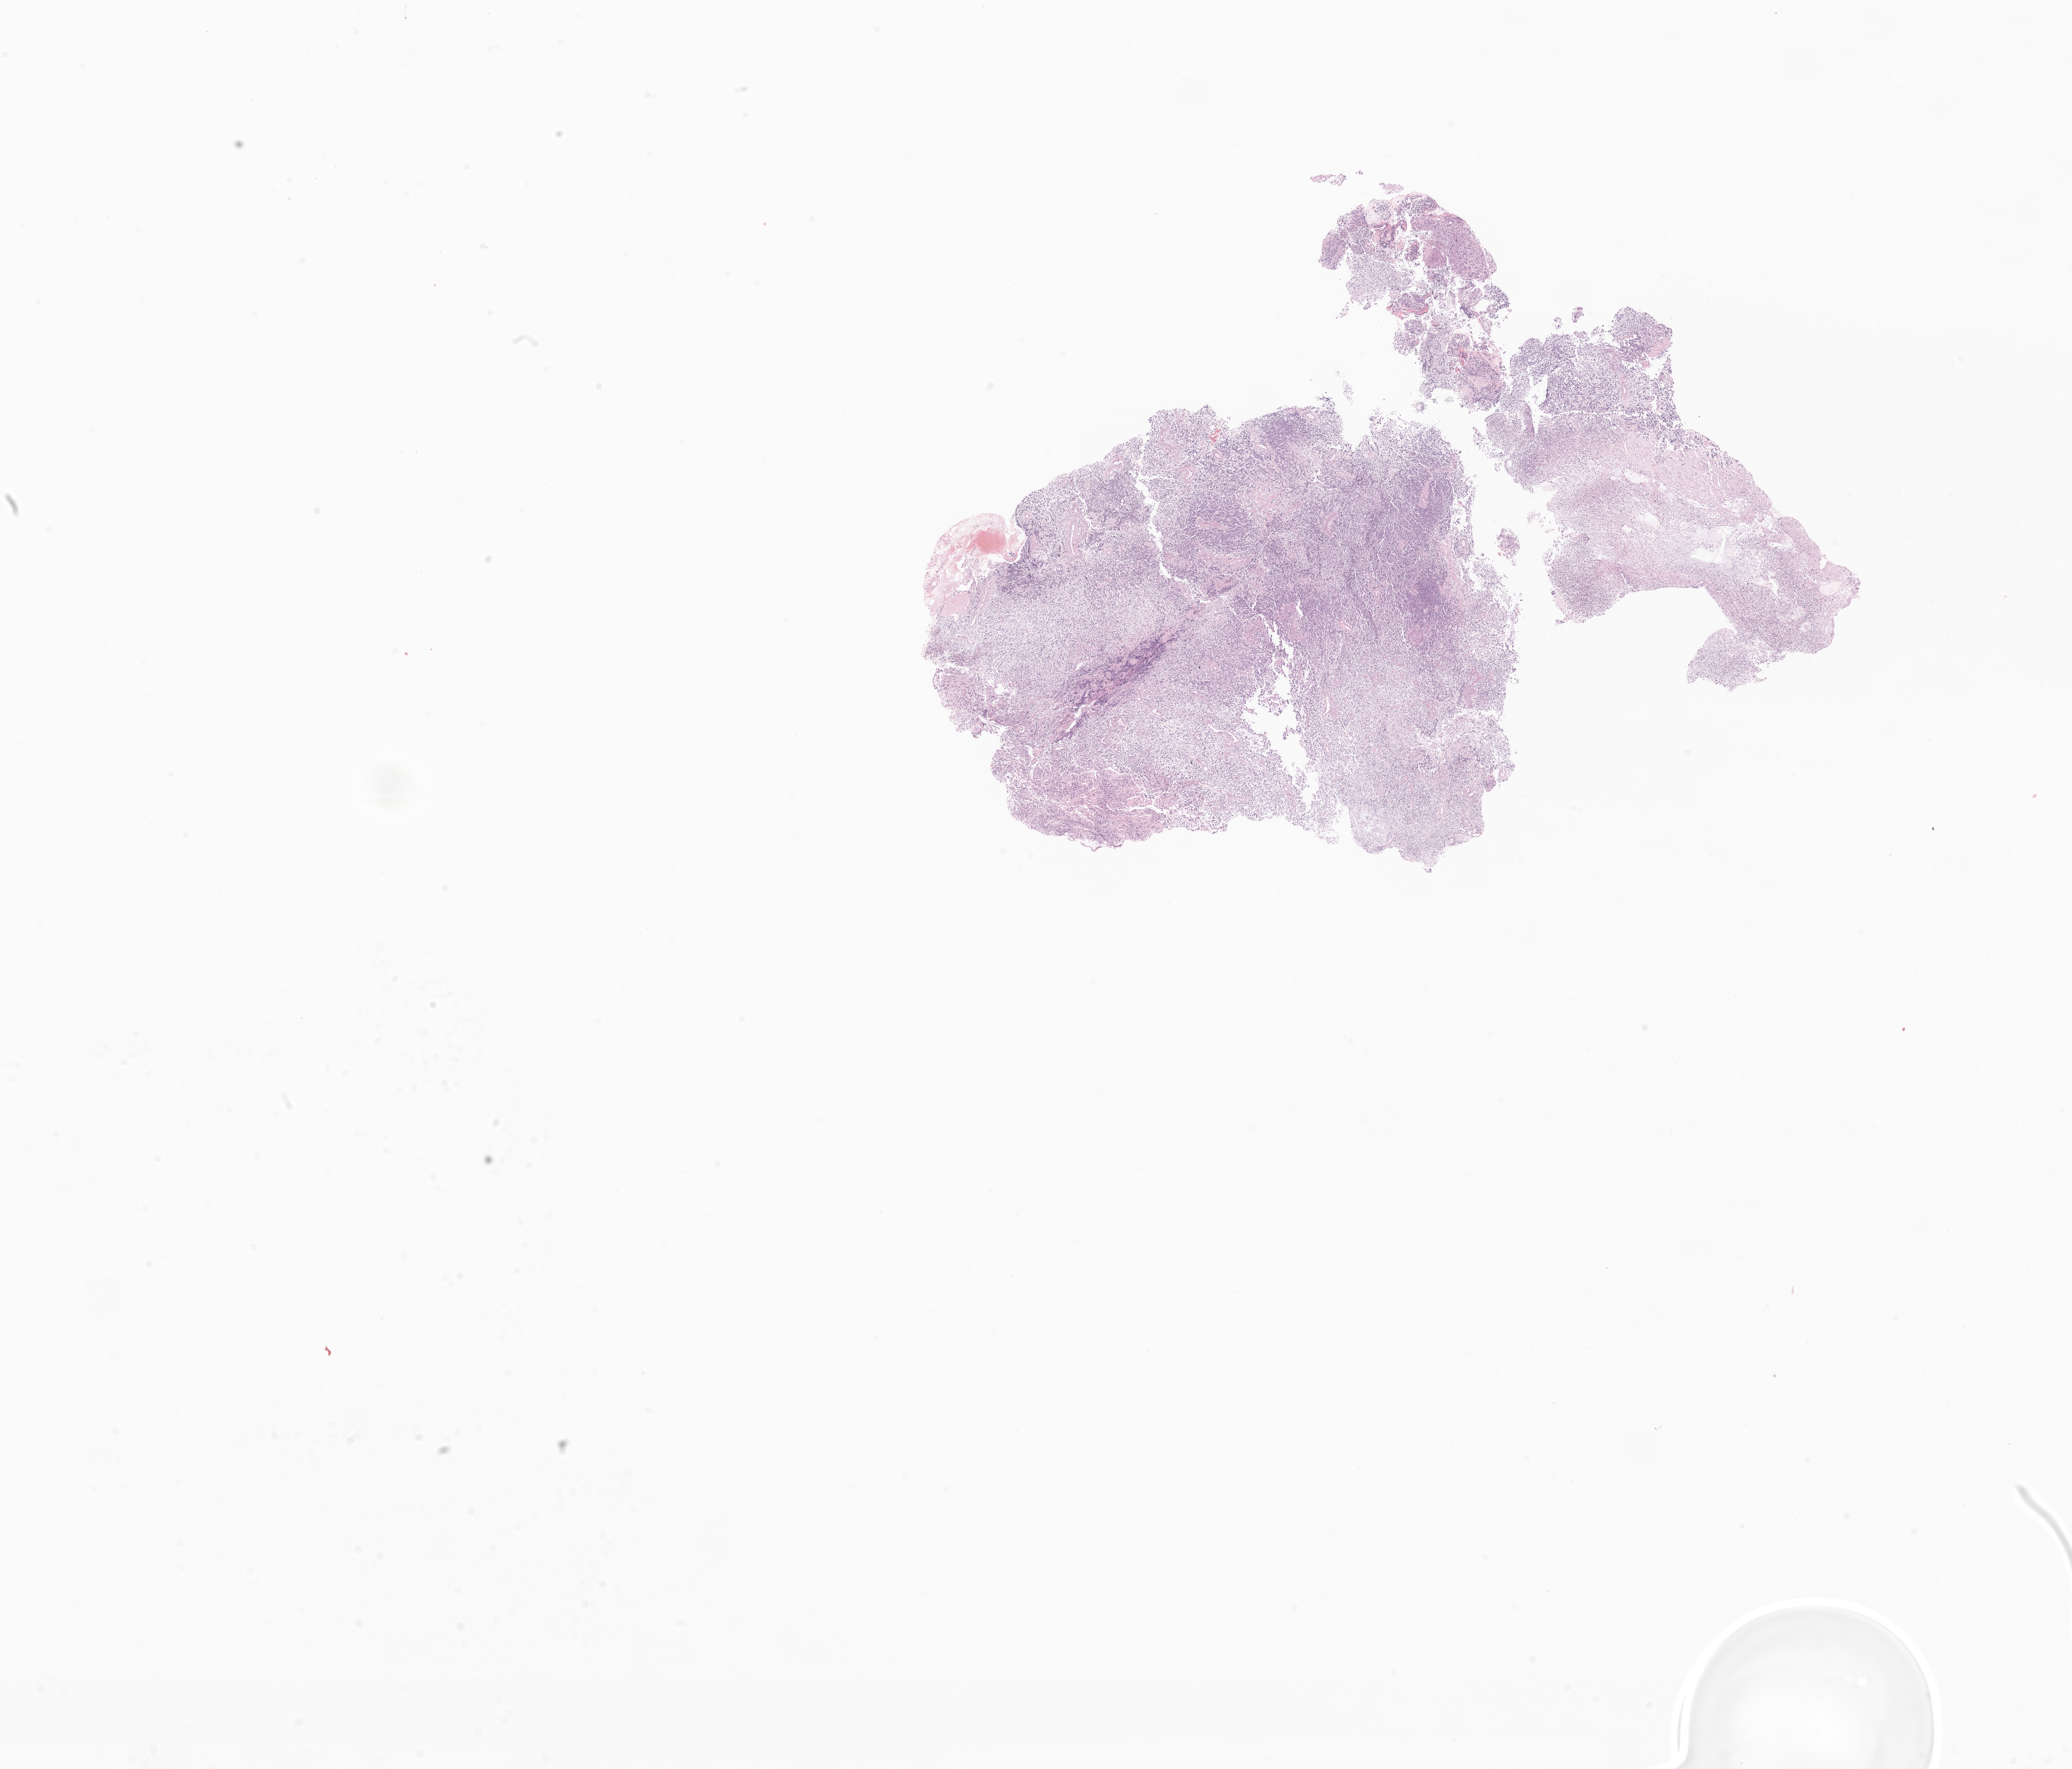
Digitized hematoxylin and eosin (H&E)-stained section of tumor tissue from the brain, whole scanned area (about 22.7 x 19.4 mm) shown as a low-resolution overview; FFPE section. Patient female; age 115 months.
- diagnosis: Medulloblastoma, NOS